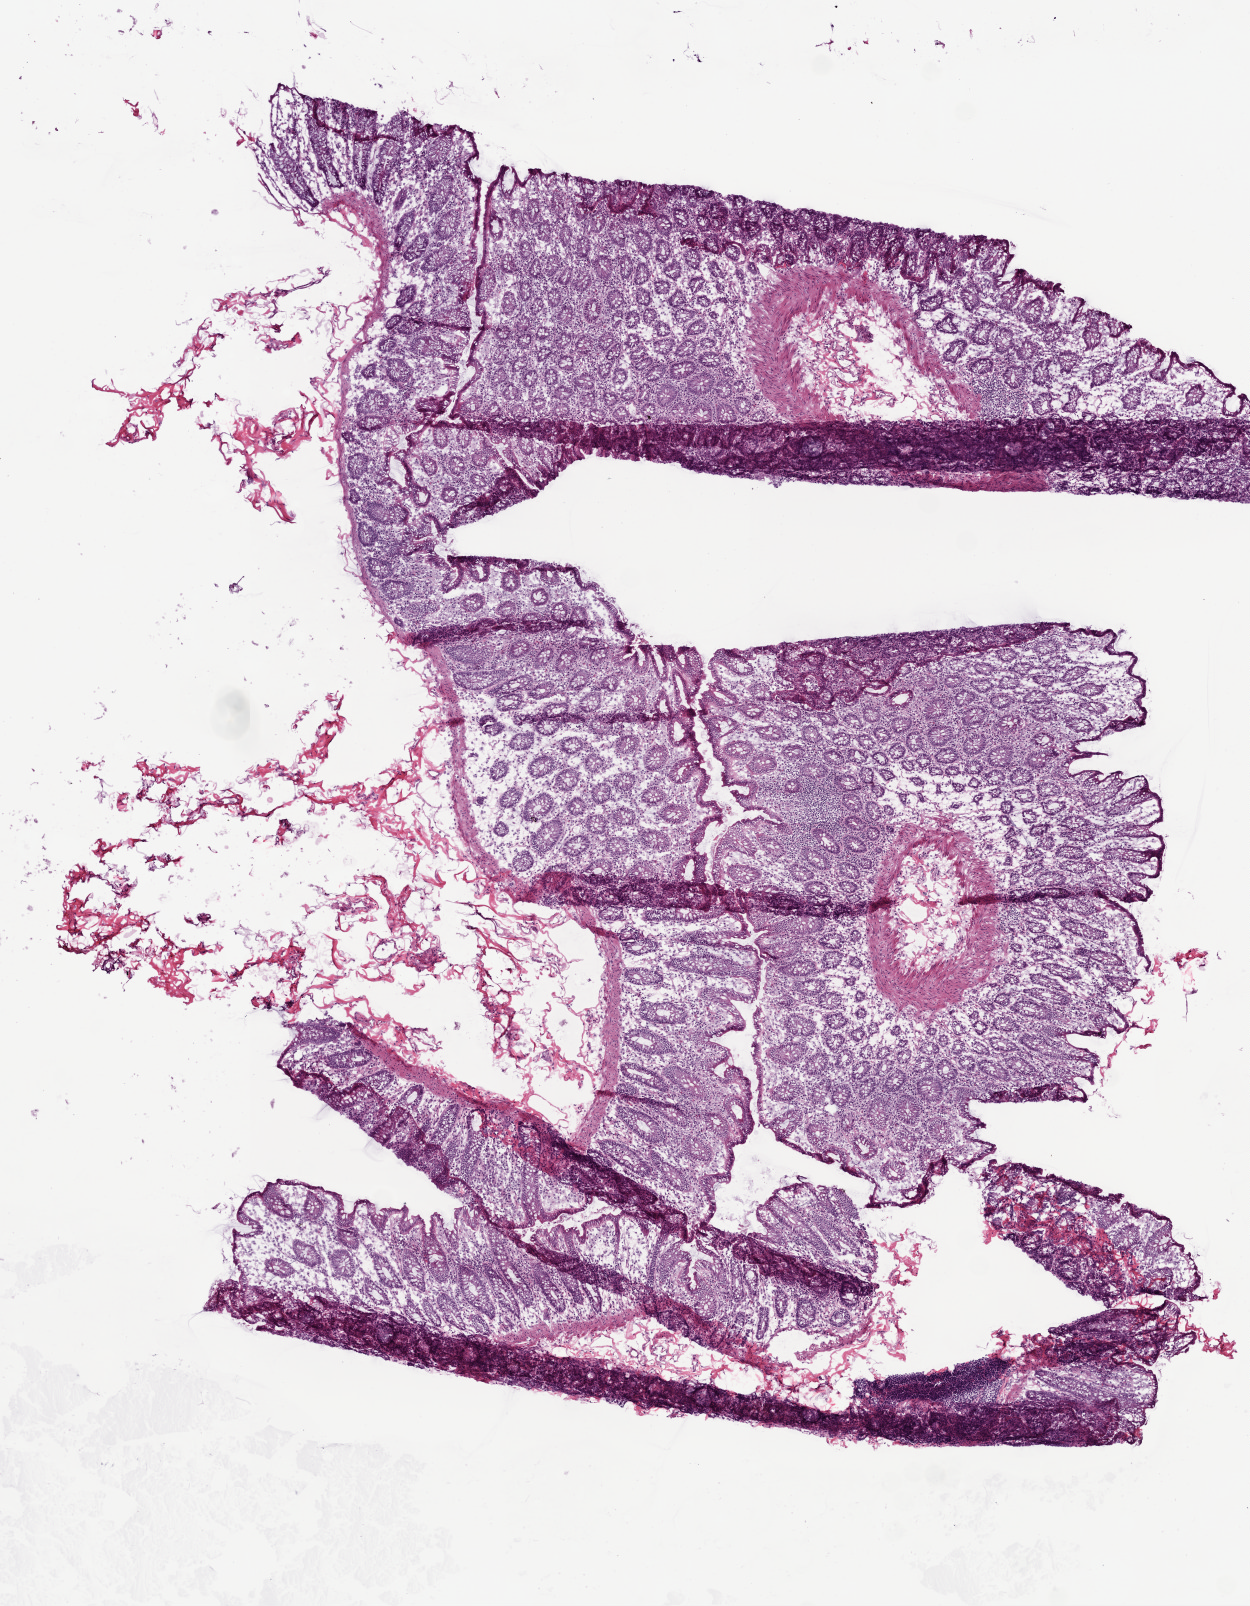
Hematoxylin and eosin (H&E) stained whole-slide image — low-resolution overview of the scanned area, about 5.0 x 6.4 mm (acquisition: 20x scan); frozen section from the top of the tissue portion; colon, solid tissue normal (non-tumour tissue) sample. Male patient; age at initial diagnosis 42 years.
• this section: solid tissue normal sample (biorepository sample class)
• patient diagnosis: Adenocarcinoma, NOS (cecum)